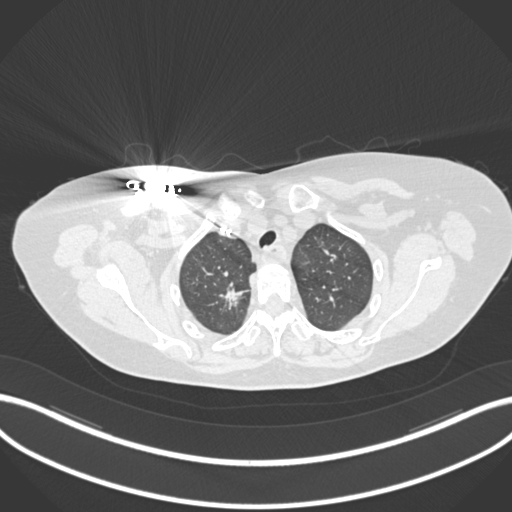
Chest CT, one axial slice. Position 150 of 176 along the scan axis. Reconstruction kernel B30f. Lung window (W 1500 / L -600 HU). 1 mm slice thickness. 512 × 512 image matrix. Female patient, age 72 years. Case-level facts recorded for this patient, not image findings: clinical TNM (as recorded): T1c N0 M0.
Outlined on this slice (bounding box drawn by a radiologist):
- lung tumour (recorded histology: adenocarcinoma): box from (x=215, y=284) to (x=251, y=317) px